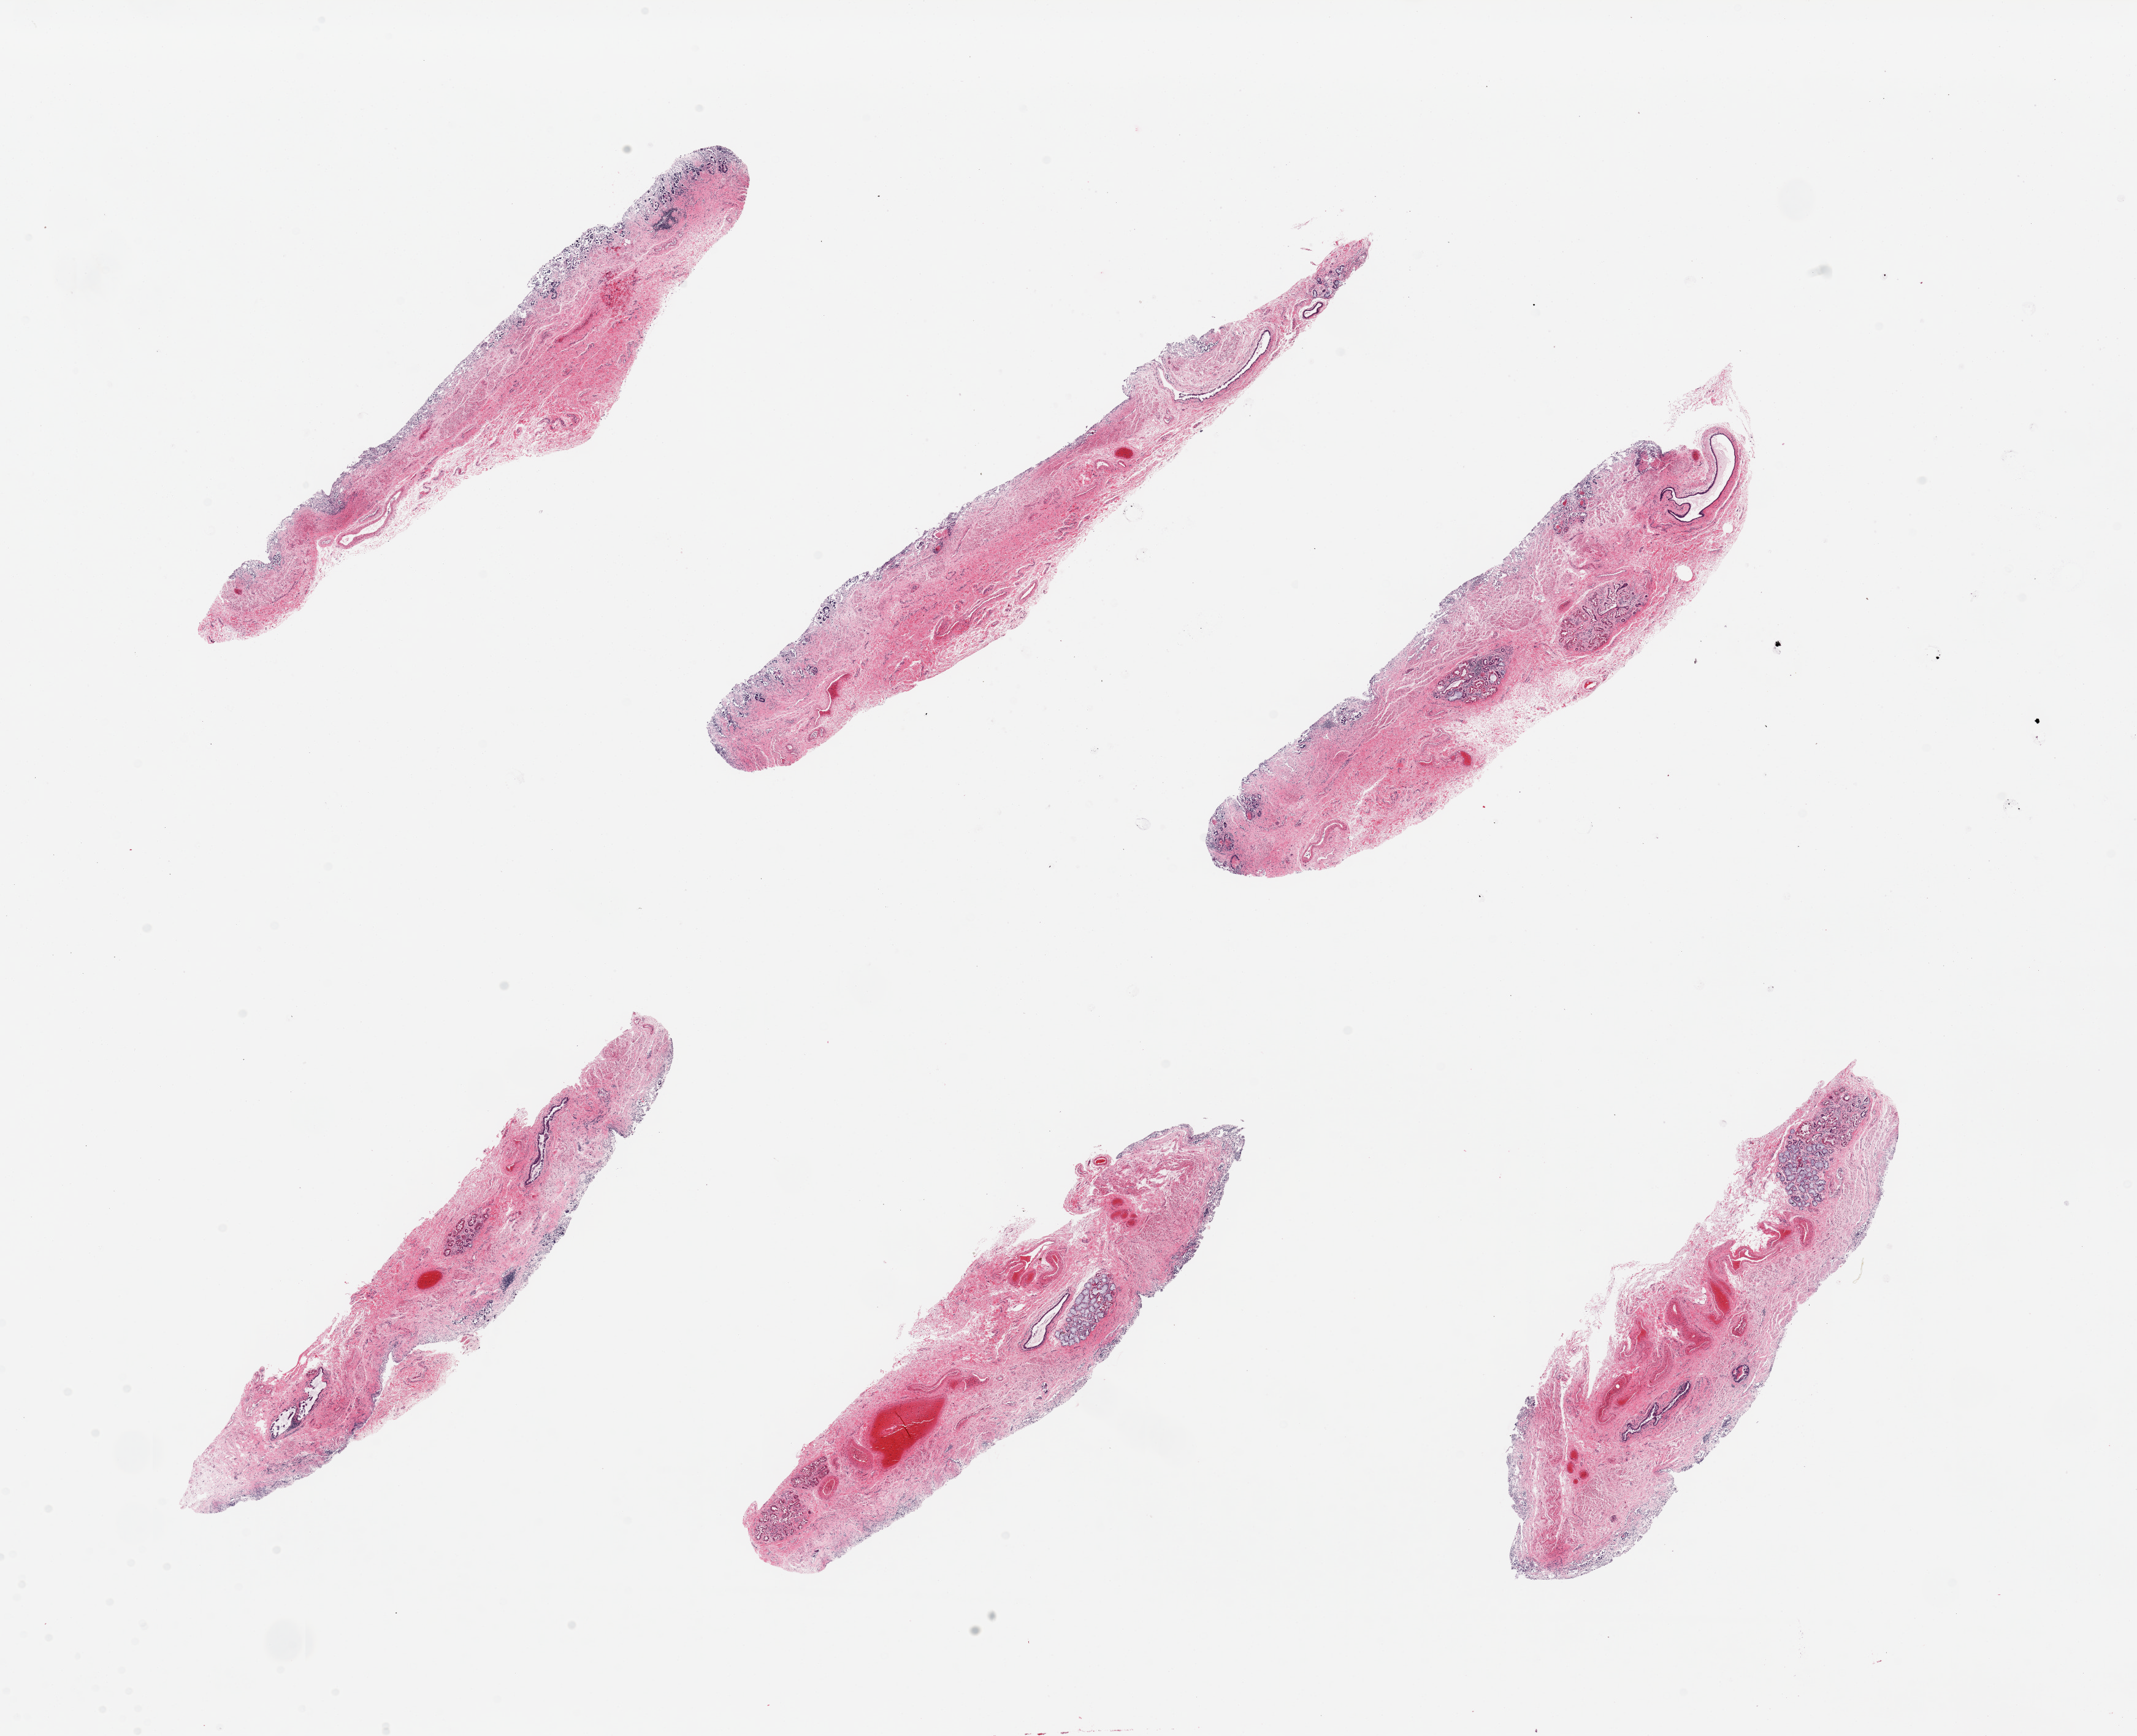
Digitized H&E-stained section, brightfield — whole scanned area (about 27.6 x 22.4 mm, slide scanned at 20x) shown as a low-resolution overview; PAXgene-fixed paraffin-embedded (PFPE) section; section of esophageal mucous membrane (target tissue); donor tissue sample. Donor sex: male.
Reviewer comment on this tissue sample: 6 pieces; totally autolyzed epithelium.